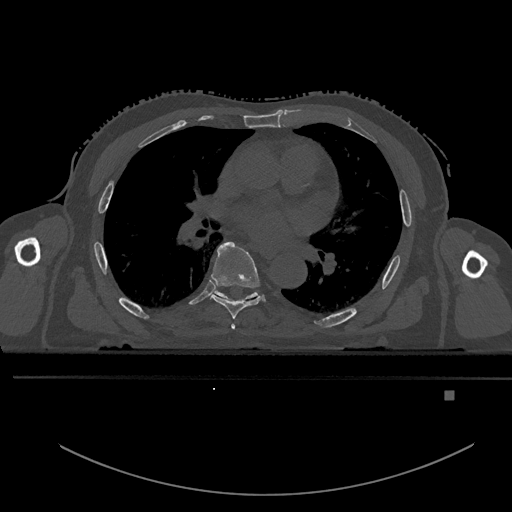
CT including the spine, one axial slice. Position 295 of 969 along the scan axis. Bone window (W 1800 / L 400 HU). 0.5 mm slice thickness. 512 × 512 image matrix, field of view 456 × 456 mm. Male patient, age 82 years. From the clinical record (not read from this slice): primary cancer: prostate; vertebrae with lytic lesions (as recorded): T11, T9, T8, T2.
Structures marked on this image (semi-automatic segmentation, software-assisted and operator-edited):
- T5 vertebra: bounding box <231,324,236,330> (left, top, right, bottom; pixels)
- T6 vertebra: <211,241,260,319>
- T7 vertebra: <214,291,256,299>